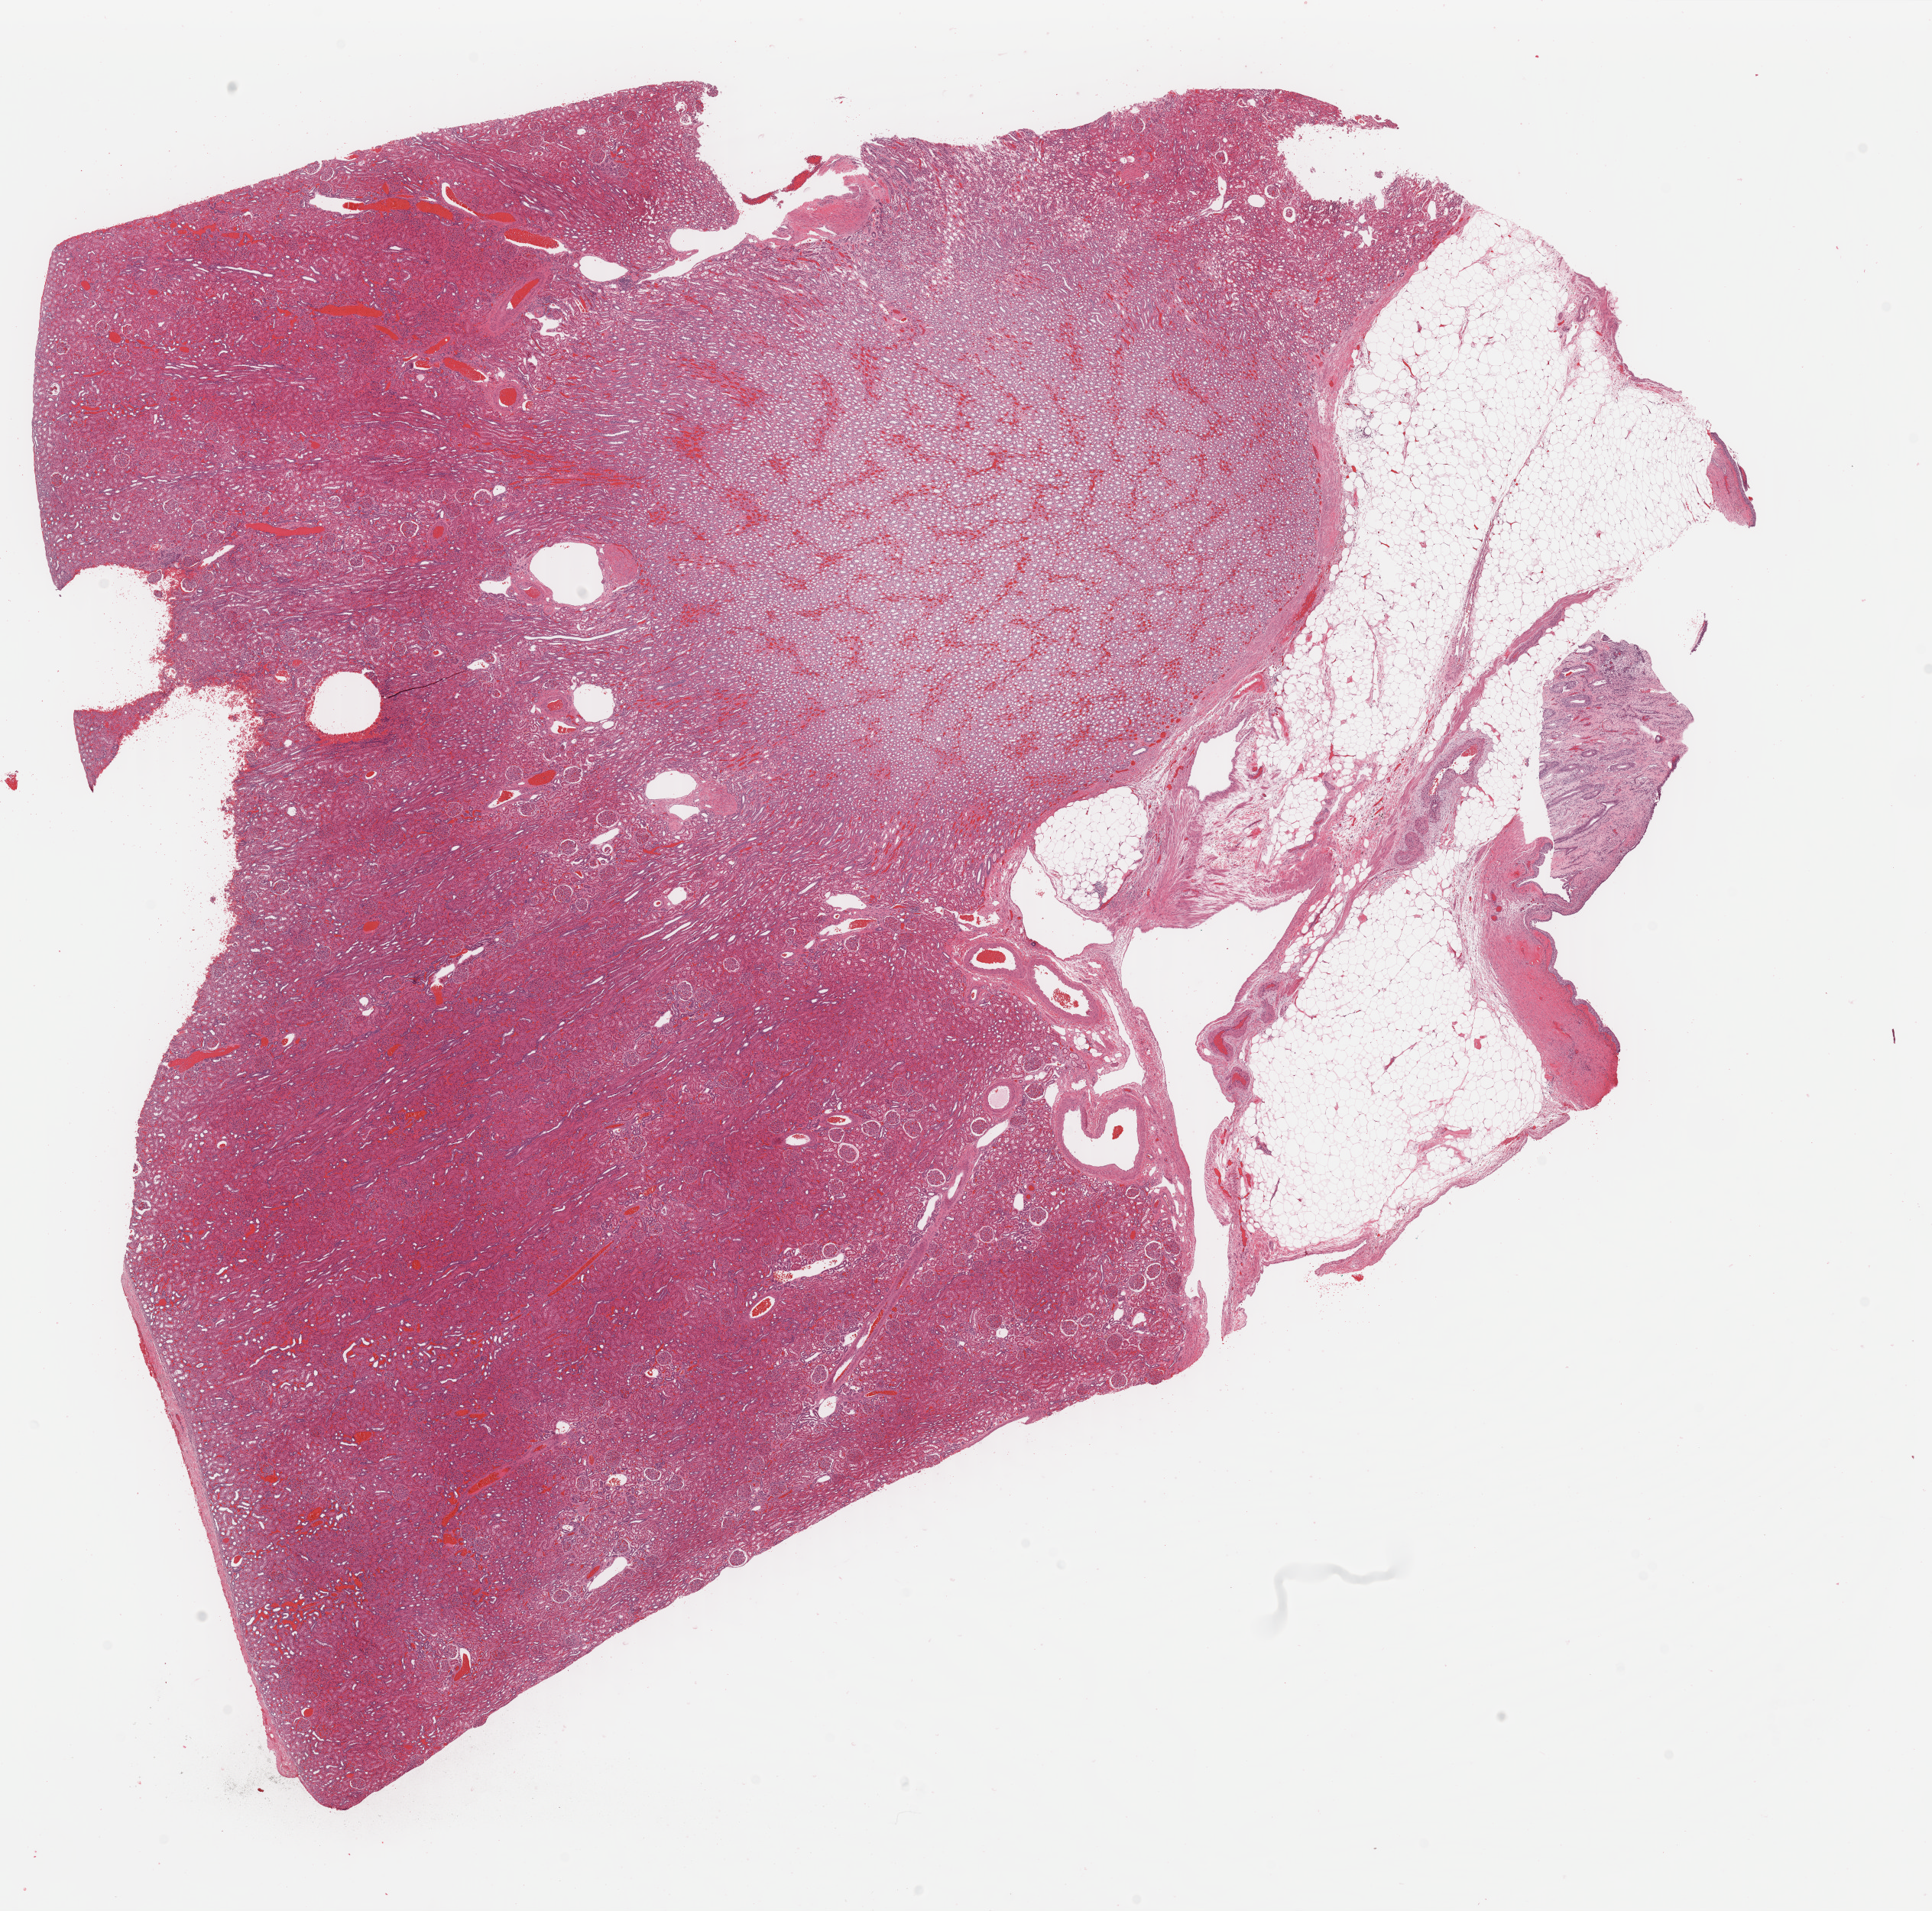
H&E-stained whole-slide image — low-resolution overview of the scanned area, about 20.0 x 19.8 mm (from a 40x scan), formalin-fixed paraffin-embedded (FFPE) diagnostic section, sample: solid tissue normal (non-tumour tissue), kidney. Patient: male, age at initial diagnosis 31 years. Composition of this section per pathologist review: tumour cells 0%, tumour nuclei 0%, normal cells 60%, stromal cells 40%, necrosis 0%. Infiltration values recorded for this section: lymphocyte infiltration 1%, monocyte infiltration 0%, neutrophil infiltration 0%.
- this section: solid tissue normal (non-tumour) sample from the same patient
- patient diagnosis: Renal cell carcinoma, chromophobe type